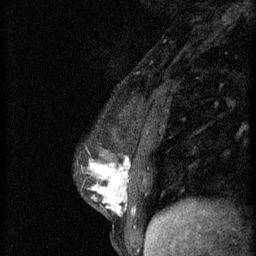
Breast MRI (dynamic contrast-enhanced), one sagittal slice. Slice 19 of 60 in the series (ordered by position). 3 images stored at this slice position (order not interpretable as contrast timing). 1.5 T. TE 4.2 ms, TR 11 ms. 256 × 256 image matrix, field of view 180 × 180 mm. Female patient, age 37 years.
Structures marked on this image (semi-automatically segmented with operator editing):
- analysis volume of interest (the breast-tissue region the enhancement analysis was run in; not a lesion): box from (x=87, y=140) to (x=174, y=221) px
- tumour enhancement mask (voxels above the 70 % enhancement threshold inside the analysis volume of interest): (x=87, y=156)–(x=130, y=217)